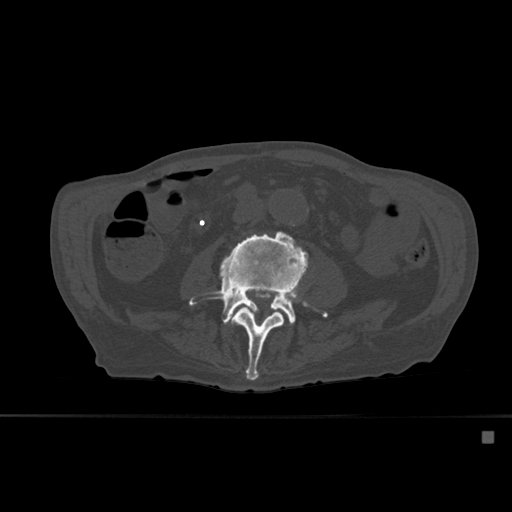
CT including the spine, one axial slice. Position 204 of 527 along the scan axis. Bone window (W 1800 / L 400 HU). 1.5 mm slice thickness. 512 × 512 image matrix. Patient: male, 78 years. From the clinical record (not read from this slice): primary cancer: prostate.
Structures marked on this image (semi-automatically segmented with operator editing):
- L3 vertebra: bounding box [x1, y1, x2, y2] px = [226, 285, 298, 381]
- L4 vertebra: [190, 231, 328, 325]